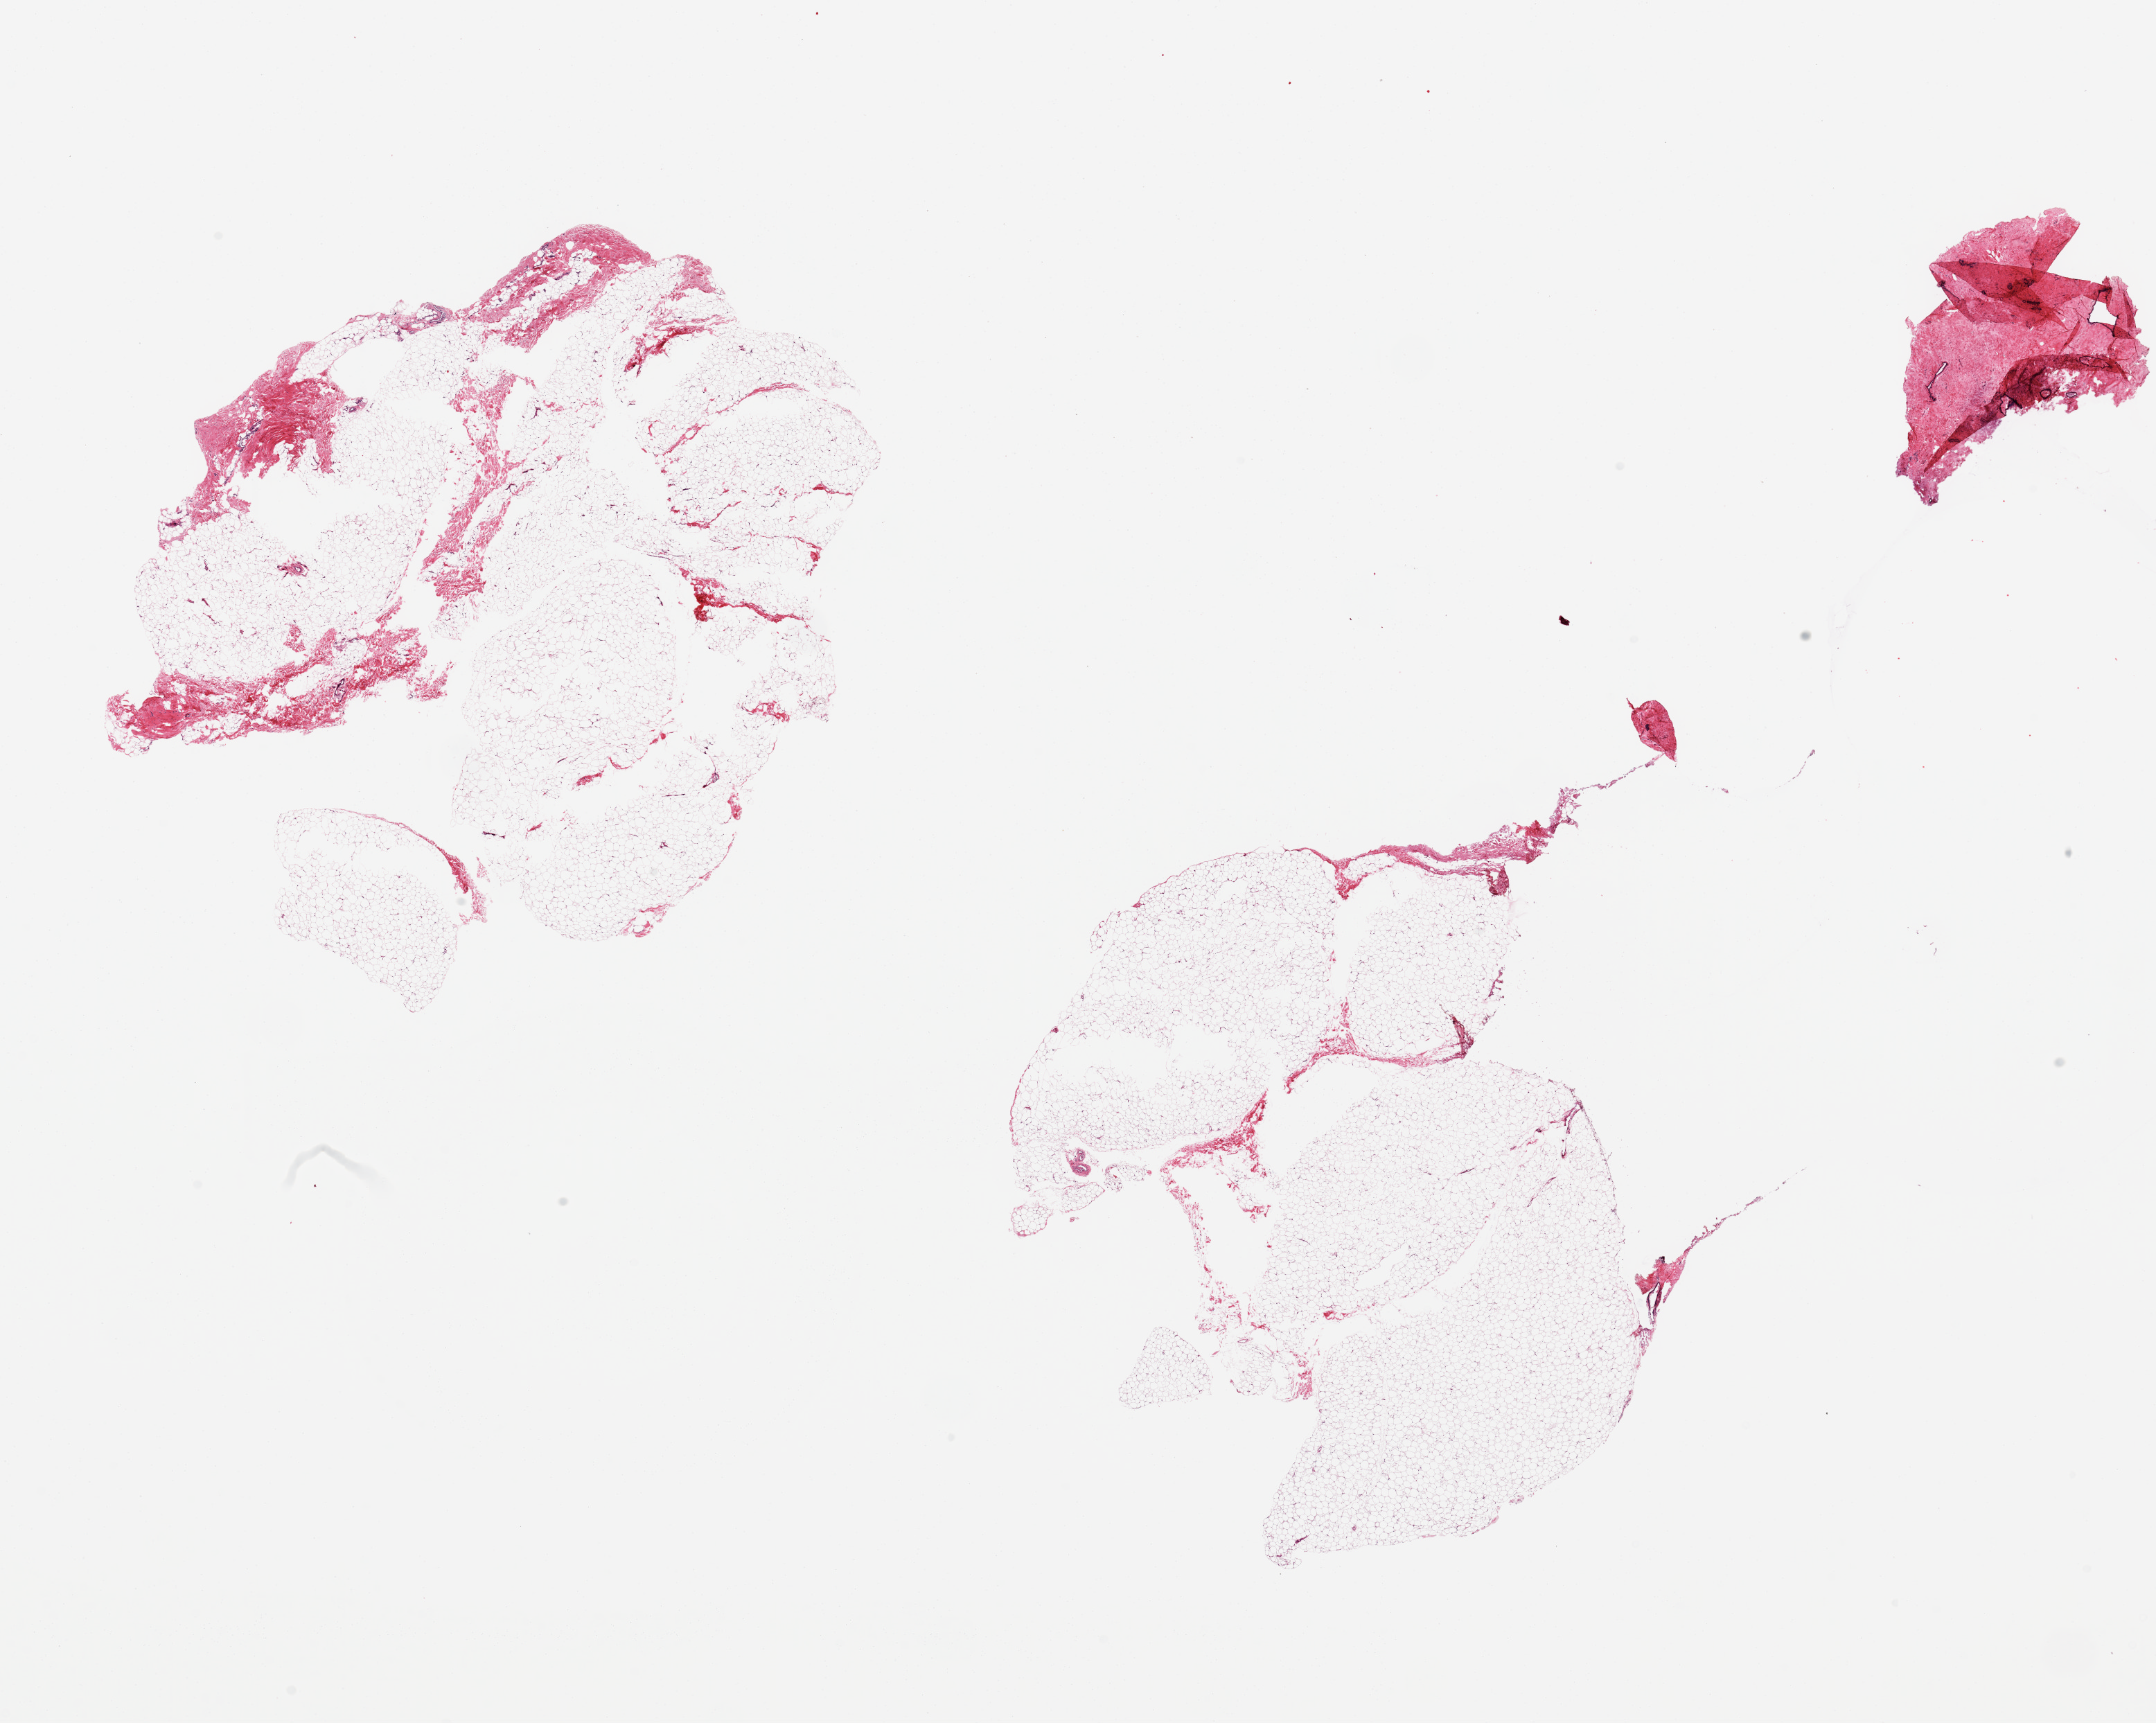
Digitized H&E-stained section, brightfield — shown as a low-resolution overview of the whole scanned area (about 24.6 x 19.7 mm, from a 20x scan), PAXgene-fixed paraffin-embedded (PFPE) section, section of breast (target tissue), donor tissue sample. Donor: male.
Pathologist's review note for this sample: 2 ~8x8 mm adipose pieces with <1% mammary tissue; 1, 3.2x2.3 mm folded fibrous piece with a few mammary ducts.